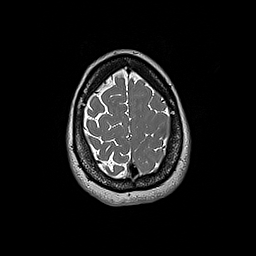
Brain MRI from a brain-tumour surgery series, one axial slice; position 49 of 192 along the scan axis; 1 mm slice thickness; 256 × 256 image matrix, field of view 250 × 250 mm. Case-level facts recorded for this patient, not image findings: histopathology: Glioblastoma; WHO grade: 4; IDH mutation: no; tumour location: Left Frontal.
Structures marked on this image (manually delineated by an expert):
- tumour: bounding box (x1, y1, x2, y2) in pixels: (161, 136, 169, 156)